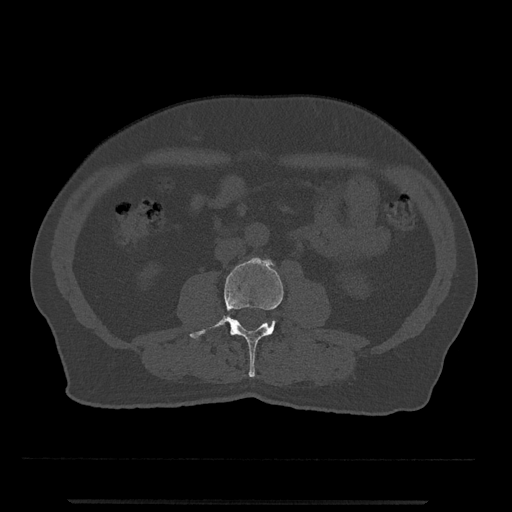
CT including the spine, one axial slice. Position 196 of 797 along the scan axis. Reconstruction kernel Br40s/3. 120 kVp. Bone window (W 1800 / L 400 HU). 512 × 512 image matrix, field of view 419 × 419 mm. Male patient, age 63 years. Case-level facts recorded for this patient, not image findings: primary cancer: prostate.
Structures marked on this image (semi-automatic segmentation, software-assisted and operator-edited):
- L3 vertebra: box from (x=189, y=257) to (x=283, y=377) px